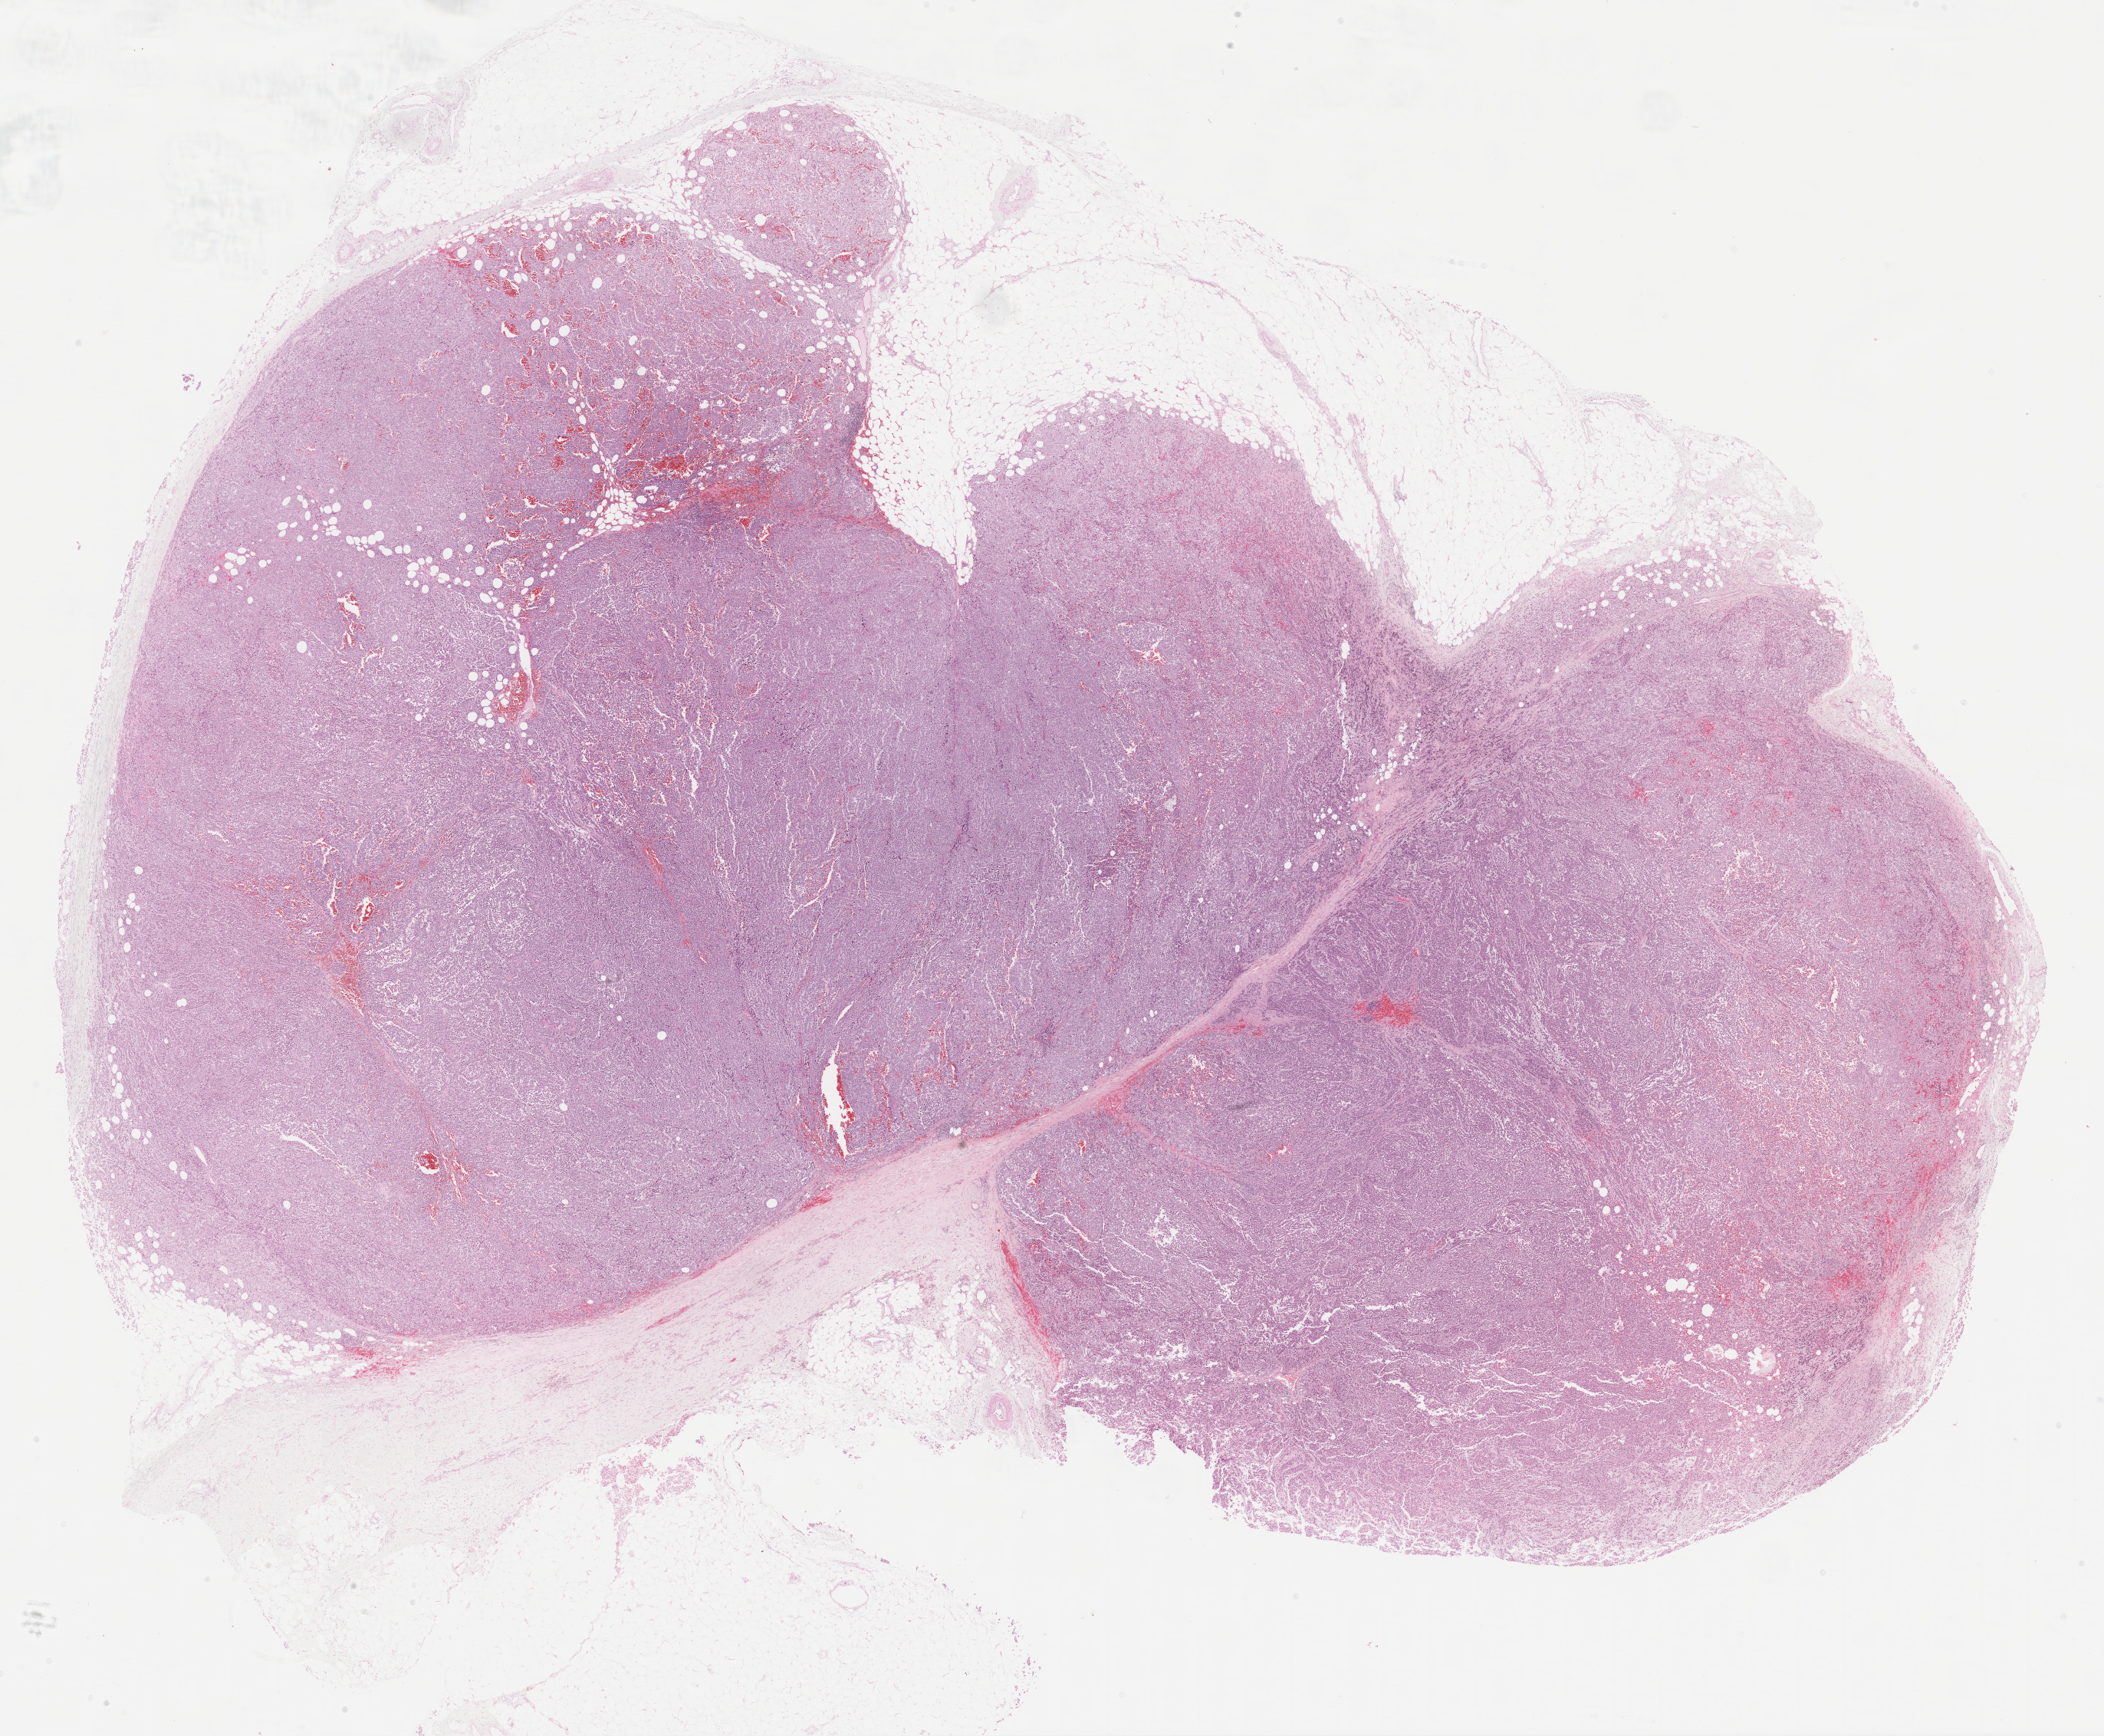
Digitized H&E tissue section (whole slide) — whole scanned area (about 22.1 x 18.3 mm) shown as a low-resolution overview, FFPE section, metastatic tumour sample, sampled site not recorded. Female, age 79 years at initial diagnosis.
- this section: metastatic tumour tissue
- patient diagnosis: Malignant melanoma, NOS